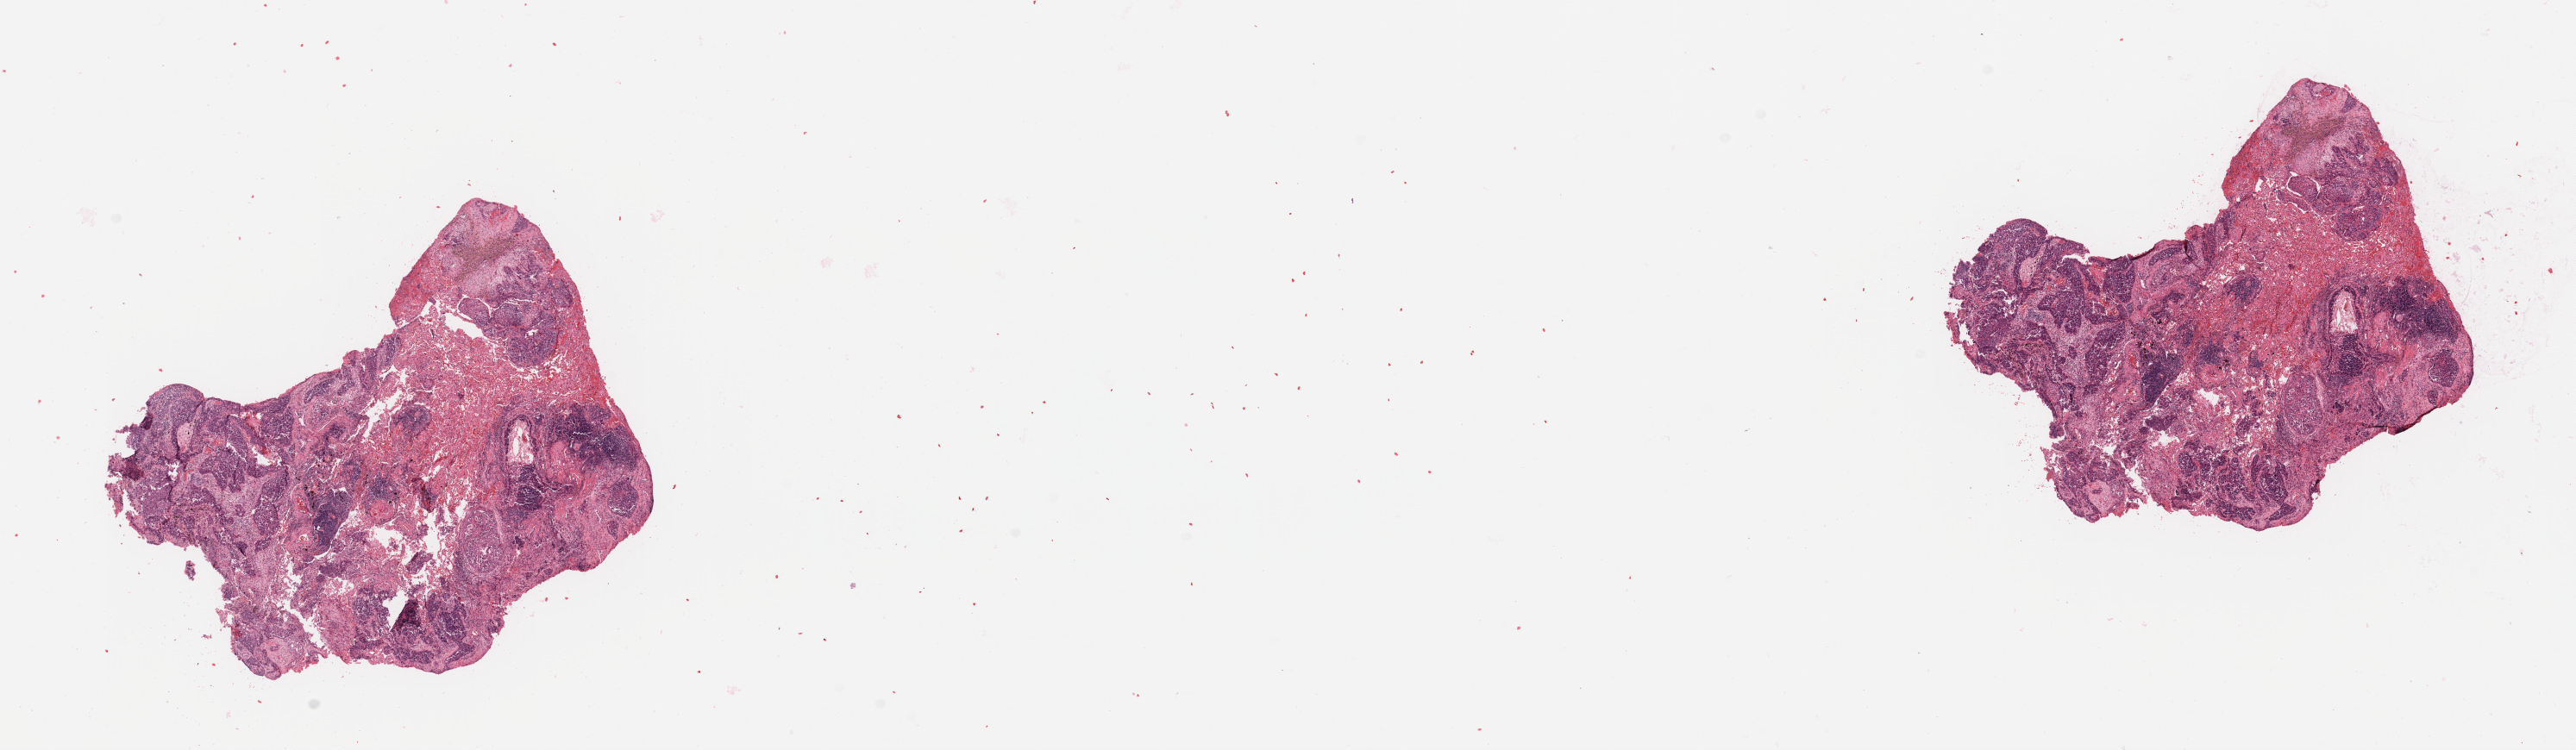
Whole-slide histology image, H&E-stained, a low-resolution overview of the entire scanned area, about 23.6 x 6.9 mm (acquisition: 20x scan). Tumour tissue sample, sampled site: lung. 64-year-old female patient. Composition of this section per pathologist review: tumour nuclei 60%, necrosis 10%.
Histologic diagnosis: Squamous cell carcinoma, NOS.